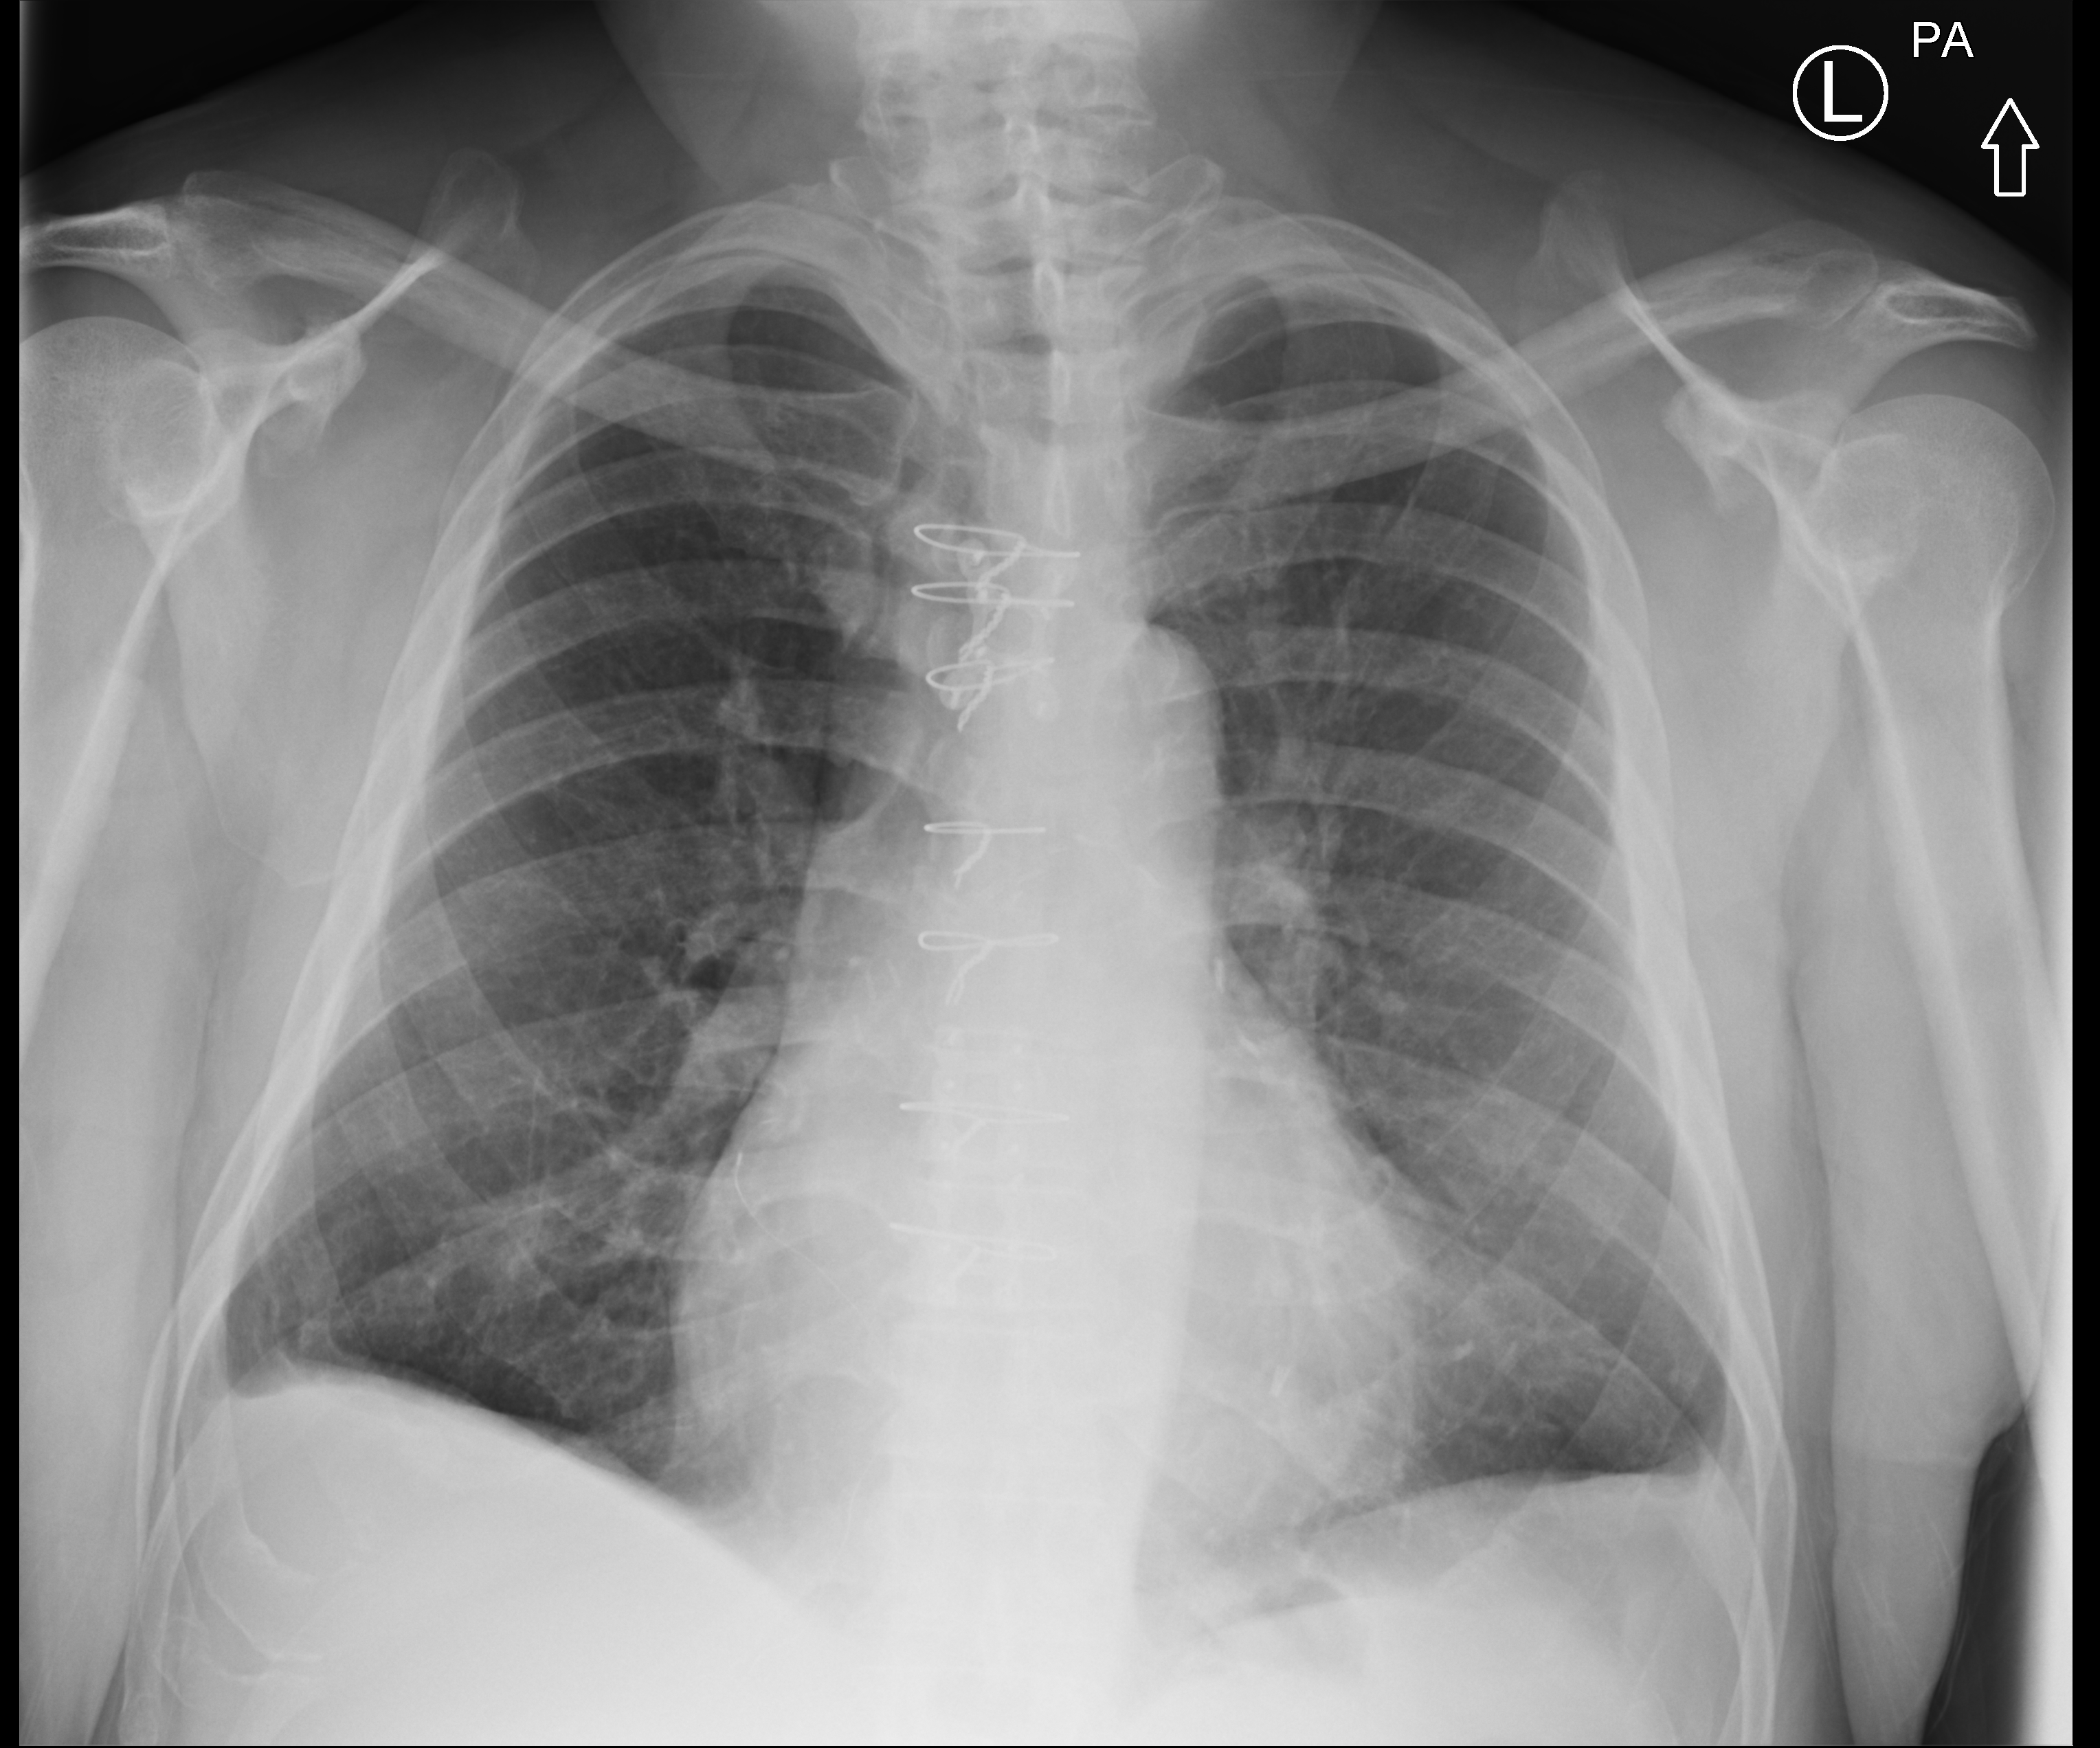
Chest radiograph (computed radiography), posteroanterior (PA) projection. Male patient hospitalised with COVID-19, age 60–74 years.
Hospital-stay facts (about this admission, not read from this image; timing relative to this image not recorded):
- other chronic lung disease (admission record): yes
- admitted to intensive care during this hospital stay: no
- mechanically ventilated during this hospital stay: no